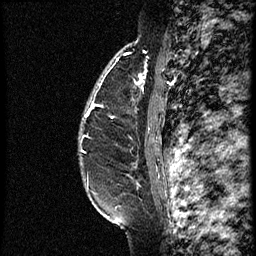
Breast MRI (dynamic contrast-enhanced), one sagittal slice. Slice 46 of 60 in the series (ordered by position). Dynamic contrast-enhanced study with each time point stored as its own series, time point 2 of 3 at this slice position (early post-contrast, ordered by acquisition time). 1.5 T. TE 4.2 ms, TR 18.9 ms. 2 mm slice thickness. 256 × 256 image matrix, field of view 200 × 200 mm. Female patient. From the clinical record (not read from this slice): setting: breast cancer imaged before/during neoadjuvant chemotherapy; receptor status: HER2-positive.
Outlined on this slice (semi-automatic segmentation, software-assisted and operator-edited):
- analysis volume of interest (the breast-tissue region the enhancement analysis was run in; not a lesion): bounding box <79,64,161,147> (left, top, right, bottom; pixels)
- tumour enhancement mask (voxels above the 100 % enhancement threshold inside the analysis volume of interest): <85,75,141,117>